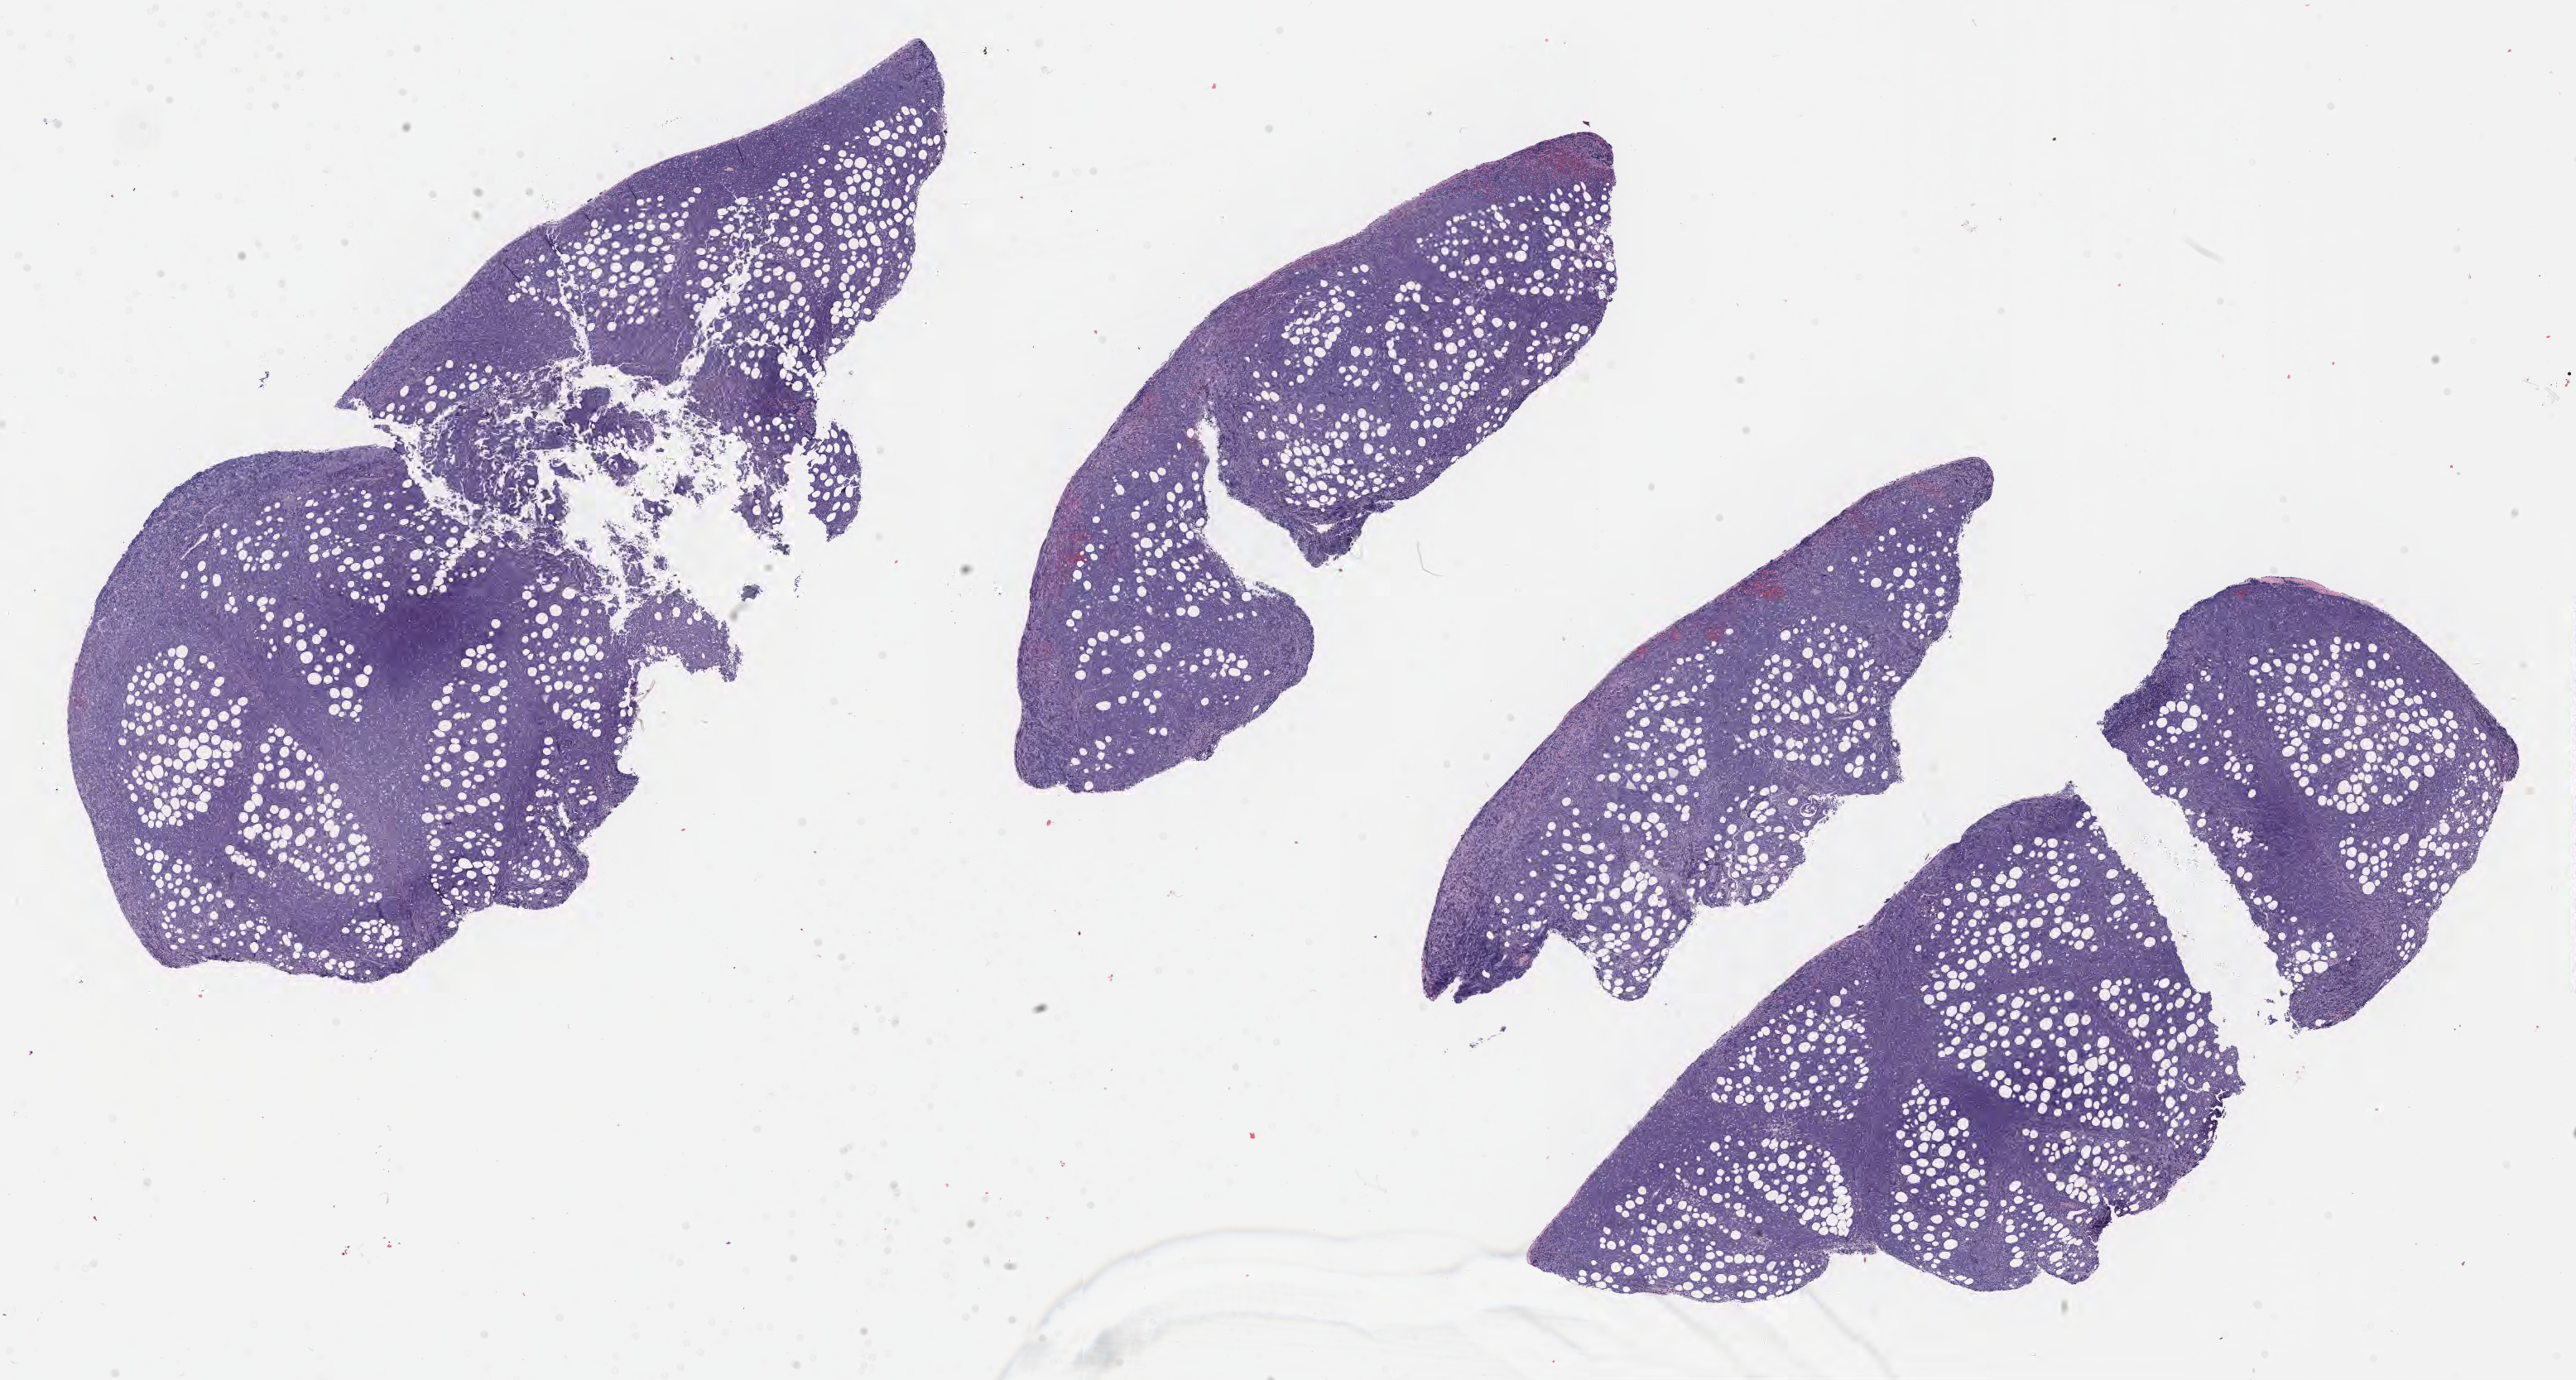
Whole-slide image, hematoxylin and eosin (H&E) stain — low-resolution overview of the scanned area, about 25.2 x 13.5 mm, tumor tissue. Patient male; 52 years old.
Histologic diagnosis: Diffuse large B-cell lymphoma, NOS.